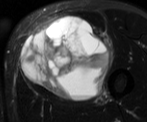
MRI of an extremity soft-tissue mass, one axial slice; position 32 of 52 along the scan axis; T2-weighted fat-saturated; MR volume resampled by the dataset authors to the PET/CT grid (not the native acquisition matrix); 3.27 mm slice thickness; 147 × 122 image matrix, field of view 144 × 119 mm. Male patient. Case-level facts recorded for this patient, not image findings: histological type: pleiomorphic liposarcoma; grade: high; site of the primary tumour: left thigh.
Structures marked on this image (expert contour drawn on MRI and transferred to this co-registered scan by the dataset authors):
- gross tumour volume including surrounding oedema: bounding box (x1, y1, x2, y2) in pixels: (21, 16, 113, 99)
- gross tumour volume (mass): (21, 16, 110, 99)